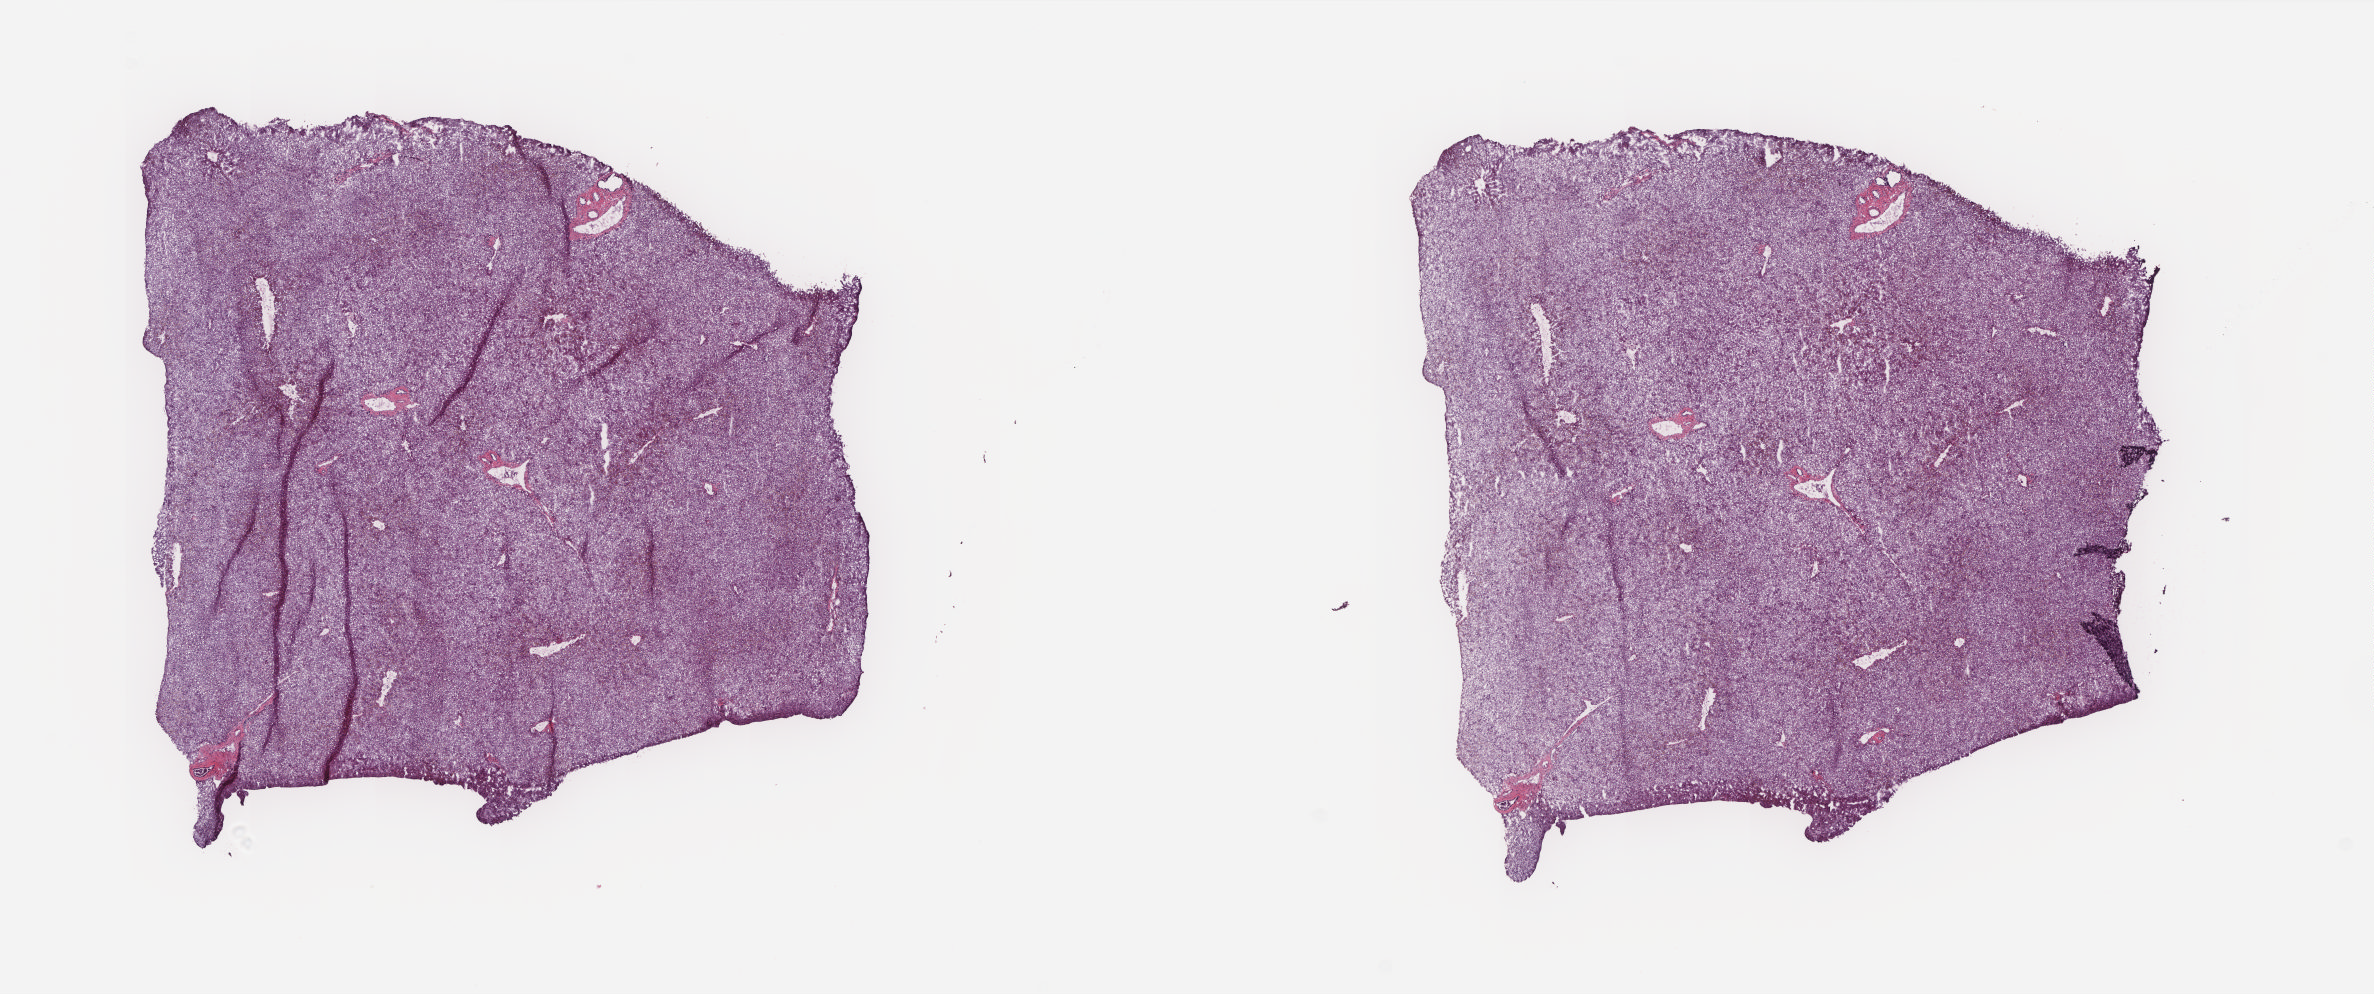
Digitized H&E-stained tissue section (whole slide) — a low-resolution overview of the entire scanned area, about 19.0 x 7.9 mm (acquisition: 20x scan), frozen section from the top of the tissue portion, liver, solid tissue normal (non-tumour tissue) sample. Patient: female, age at initial diagnosis 78 years. Composition of this section per pathologist review: tumour cells 0%, tumour nuclei 0%, normal cells 90%, stromal cells 10%, necrosis 0%. Infiltration values recorded for this section: lymphocyte infiltration 1%, monocyte infiltration 1%, neutrophil infiltration 0%.
This section: solid tissue normal (non-tumour) sample from the same patient. Patient diagnosis: Hepatocellular carcinoma, NOS.